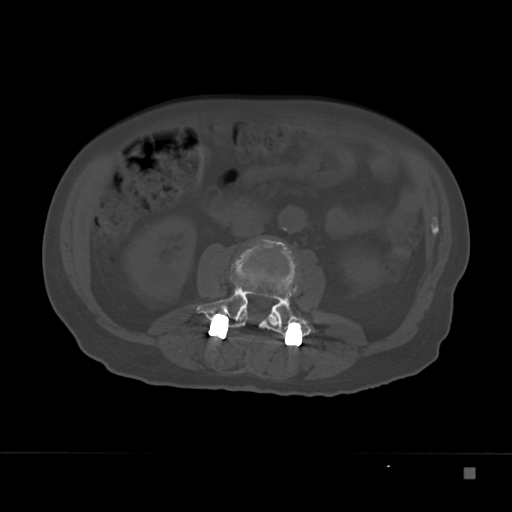
CT including the spine, one axial slice. Slice 75 of 332 in the series (ordered by position). Reconstruction kernel Br40s. 120 kVp. Bone window (W 1800 / L 400 HU). 1.5 mm slice thickness. 512 × 512 image matrix, field of view 389 × 389 mm. Patient: male, 72 years. Case-level facts recorded for this patient, not image findings: primary cancer: skeletal.
Annotated regions visible in this slice (semi-automatically segmented with operator editing):
- L2 vertebra: bounding box (x1, y1, x2, y2) in pixels: (239, 292, 283, 328)
- L3 vertebra: (196, 237, 312, 336)